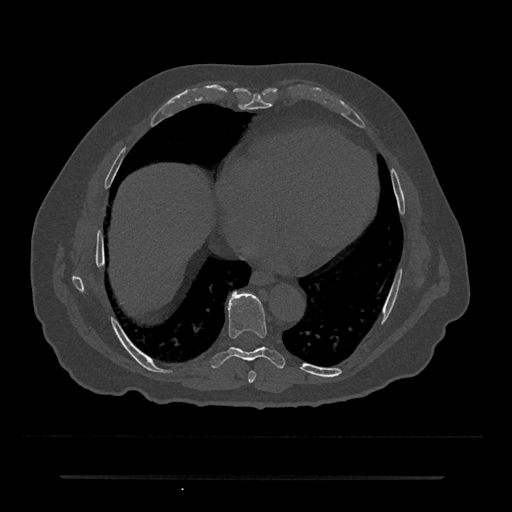
CT including the spine, one axial slice. Position 332 of 797 along the scan axis. Reconstruction kernel Br40s/3. Bone window (W 1800 / L 400 HU). 0.5 mm slice thickness. 512 × 512 image matrix. Patient: male, 69 years. From the clinical record (not read from this slice): primary cancer: prostate.
Structures marked on this image (semi-automatically segmented with operator editing):
- T7 vertebra: bounding box (x1, y1, x2, y2) in pixels: (248, 371, 256, 383)
- T8 vertebra: (211, 291, 285, 369)